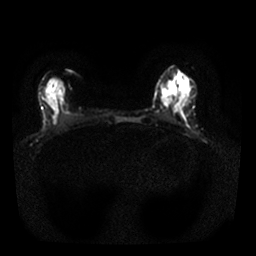
Breast MRI, one axial slice. Slice 9 of 25 in the series (ordered by position). Diffusion-weighted series; image 2 of 4 stored at this slice position (different b-values; order by instance number). 1.5 T. 4 mm slice thickness. 256 × 256 image matrix, field of view 310 × 310 mm. Female patient.
Outlined on this slice (expert manual segmentation):
- tumour on diffusion-weighted imaging: box from (x=162, y=82) to (x=175, y=106) px